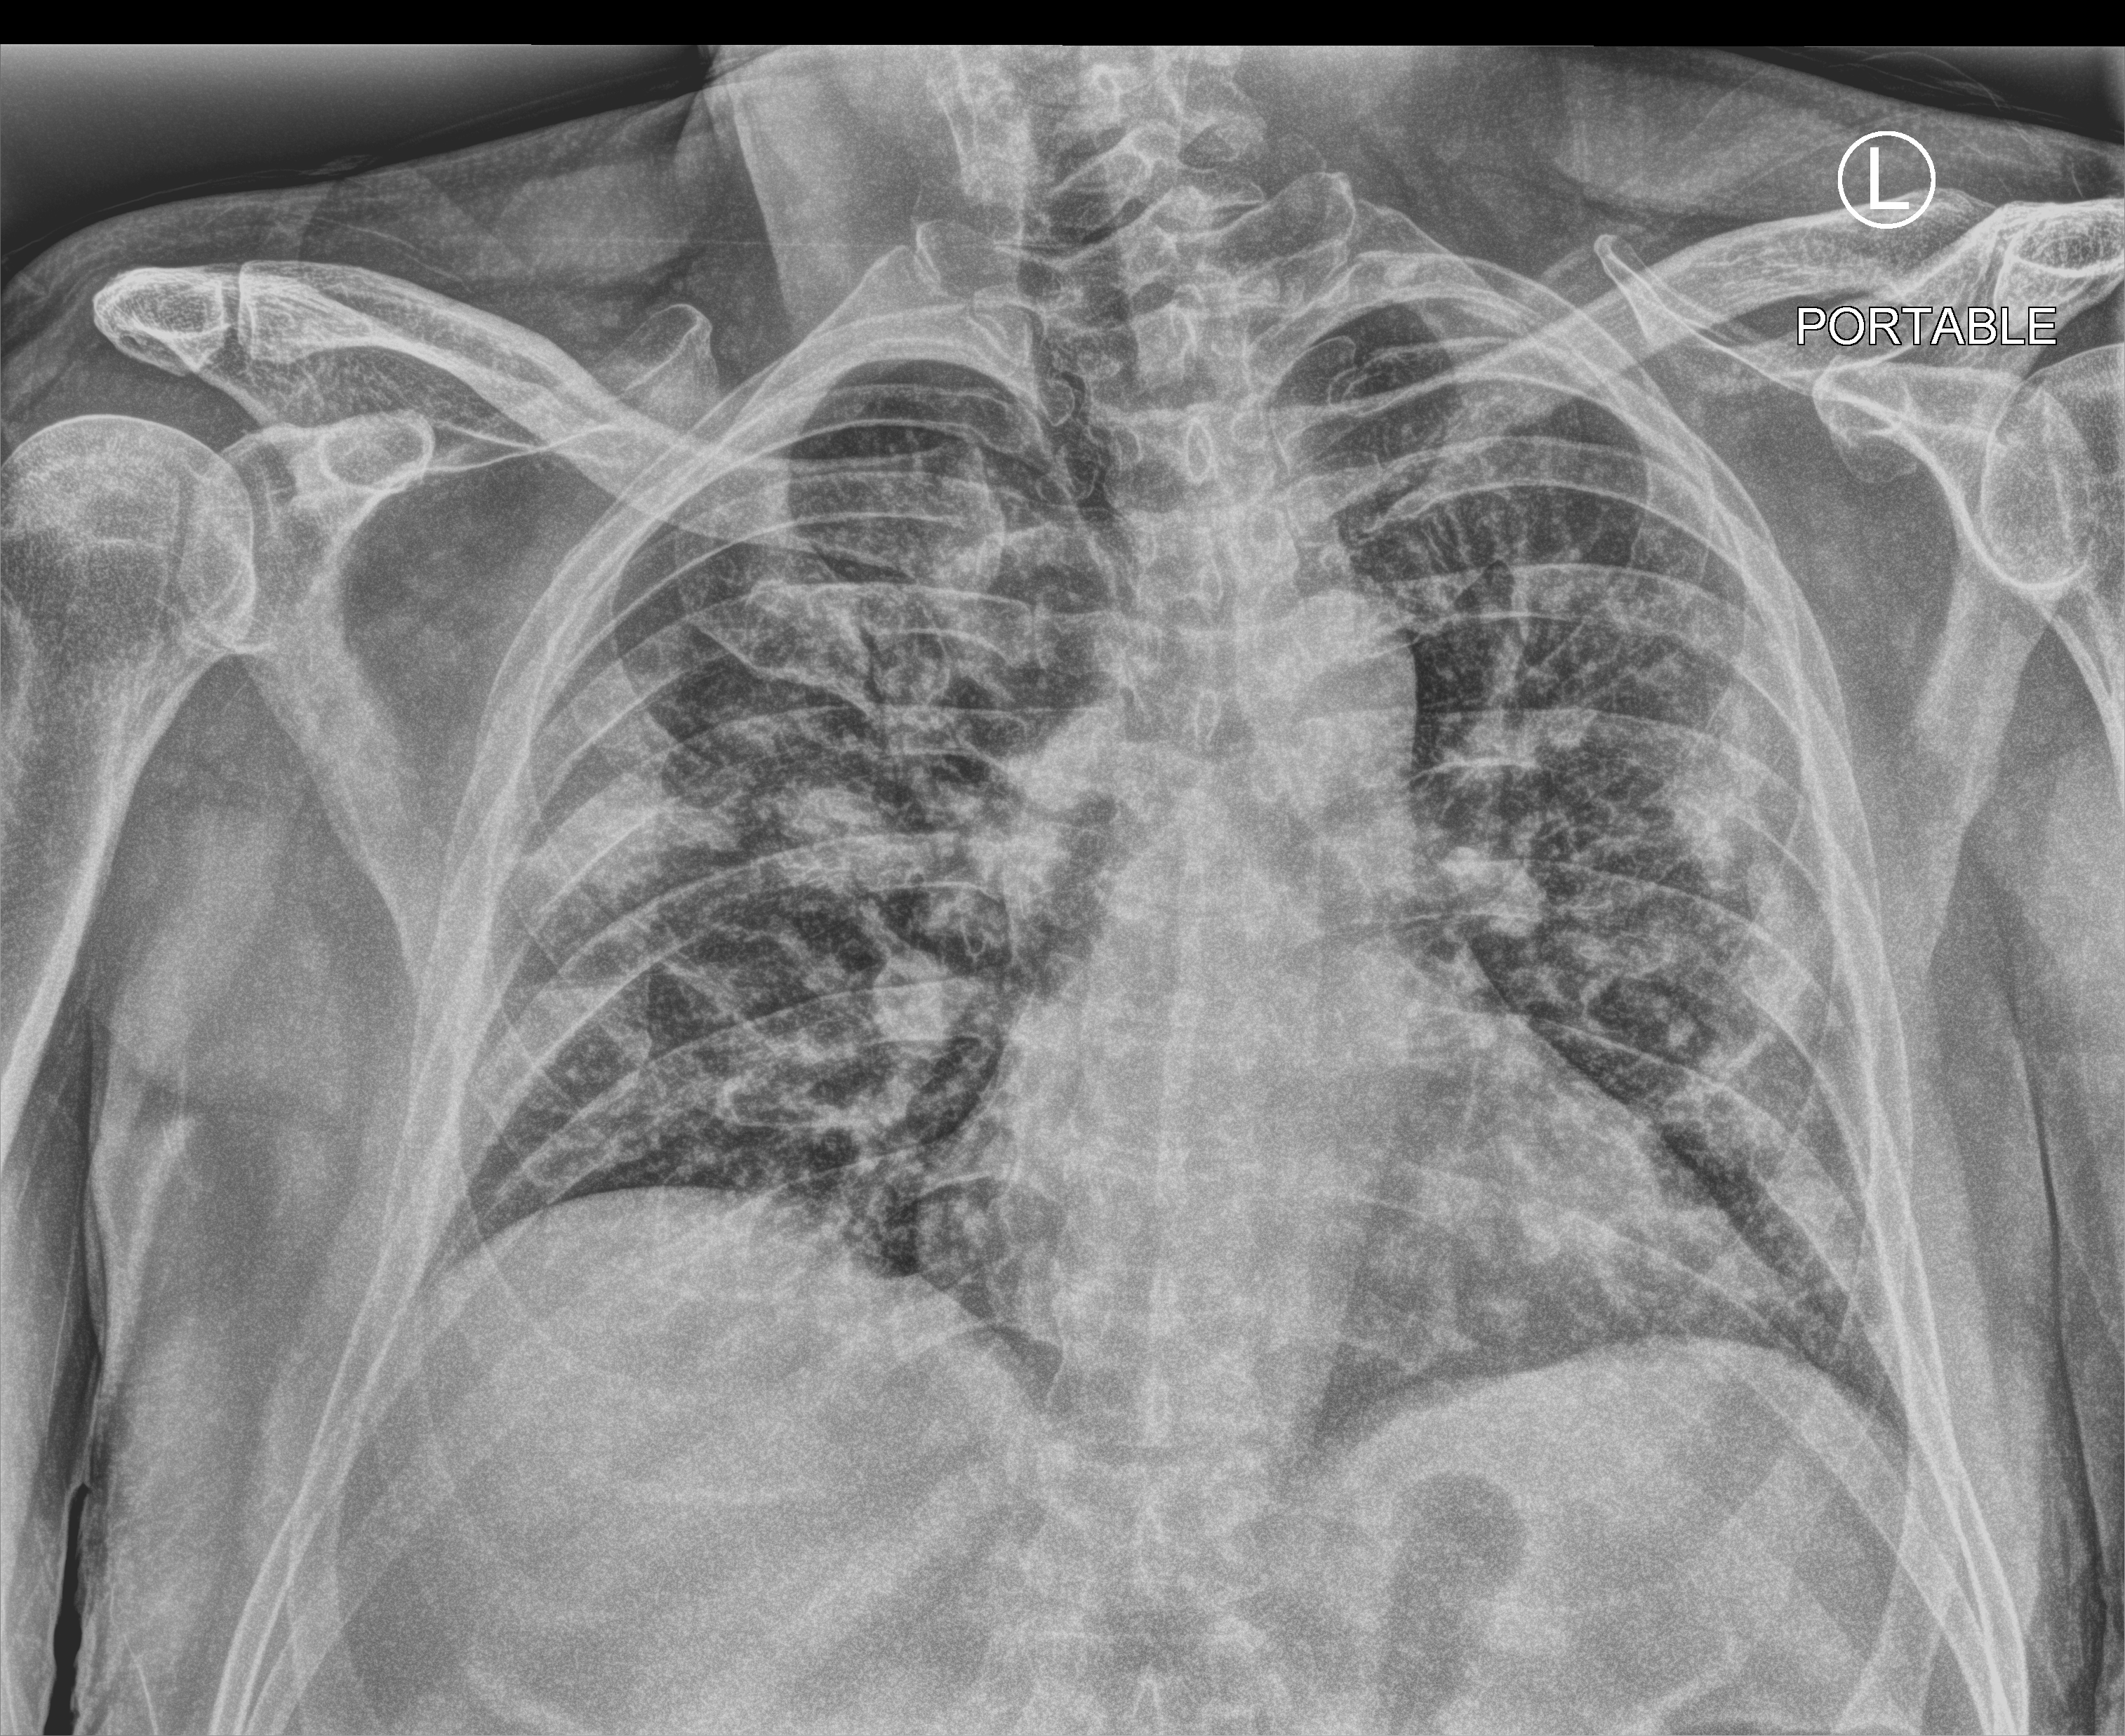
Chest X-ray (portable), anteroposterior (AP) projection. Patient hospitalised with COVID-19; male, aged 18–59 years.
From the hospital-stay record, not from the radiograph (when in the stay this image was taken is not recorded):
- admitted to intensive care during this hospital stay: yes
- mechanically ventilated during this hospital stay: yes
- diabetes (admission record): no